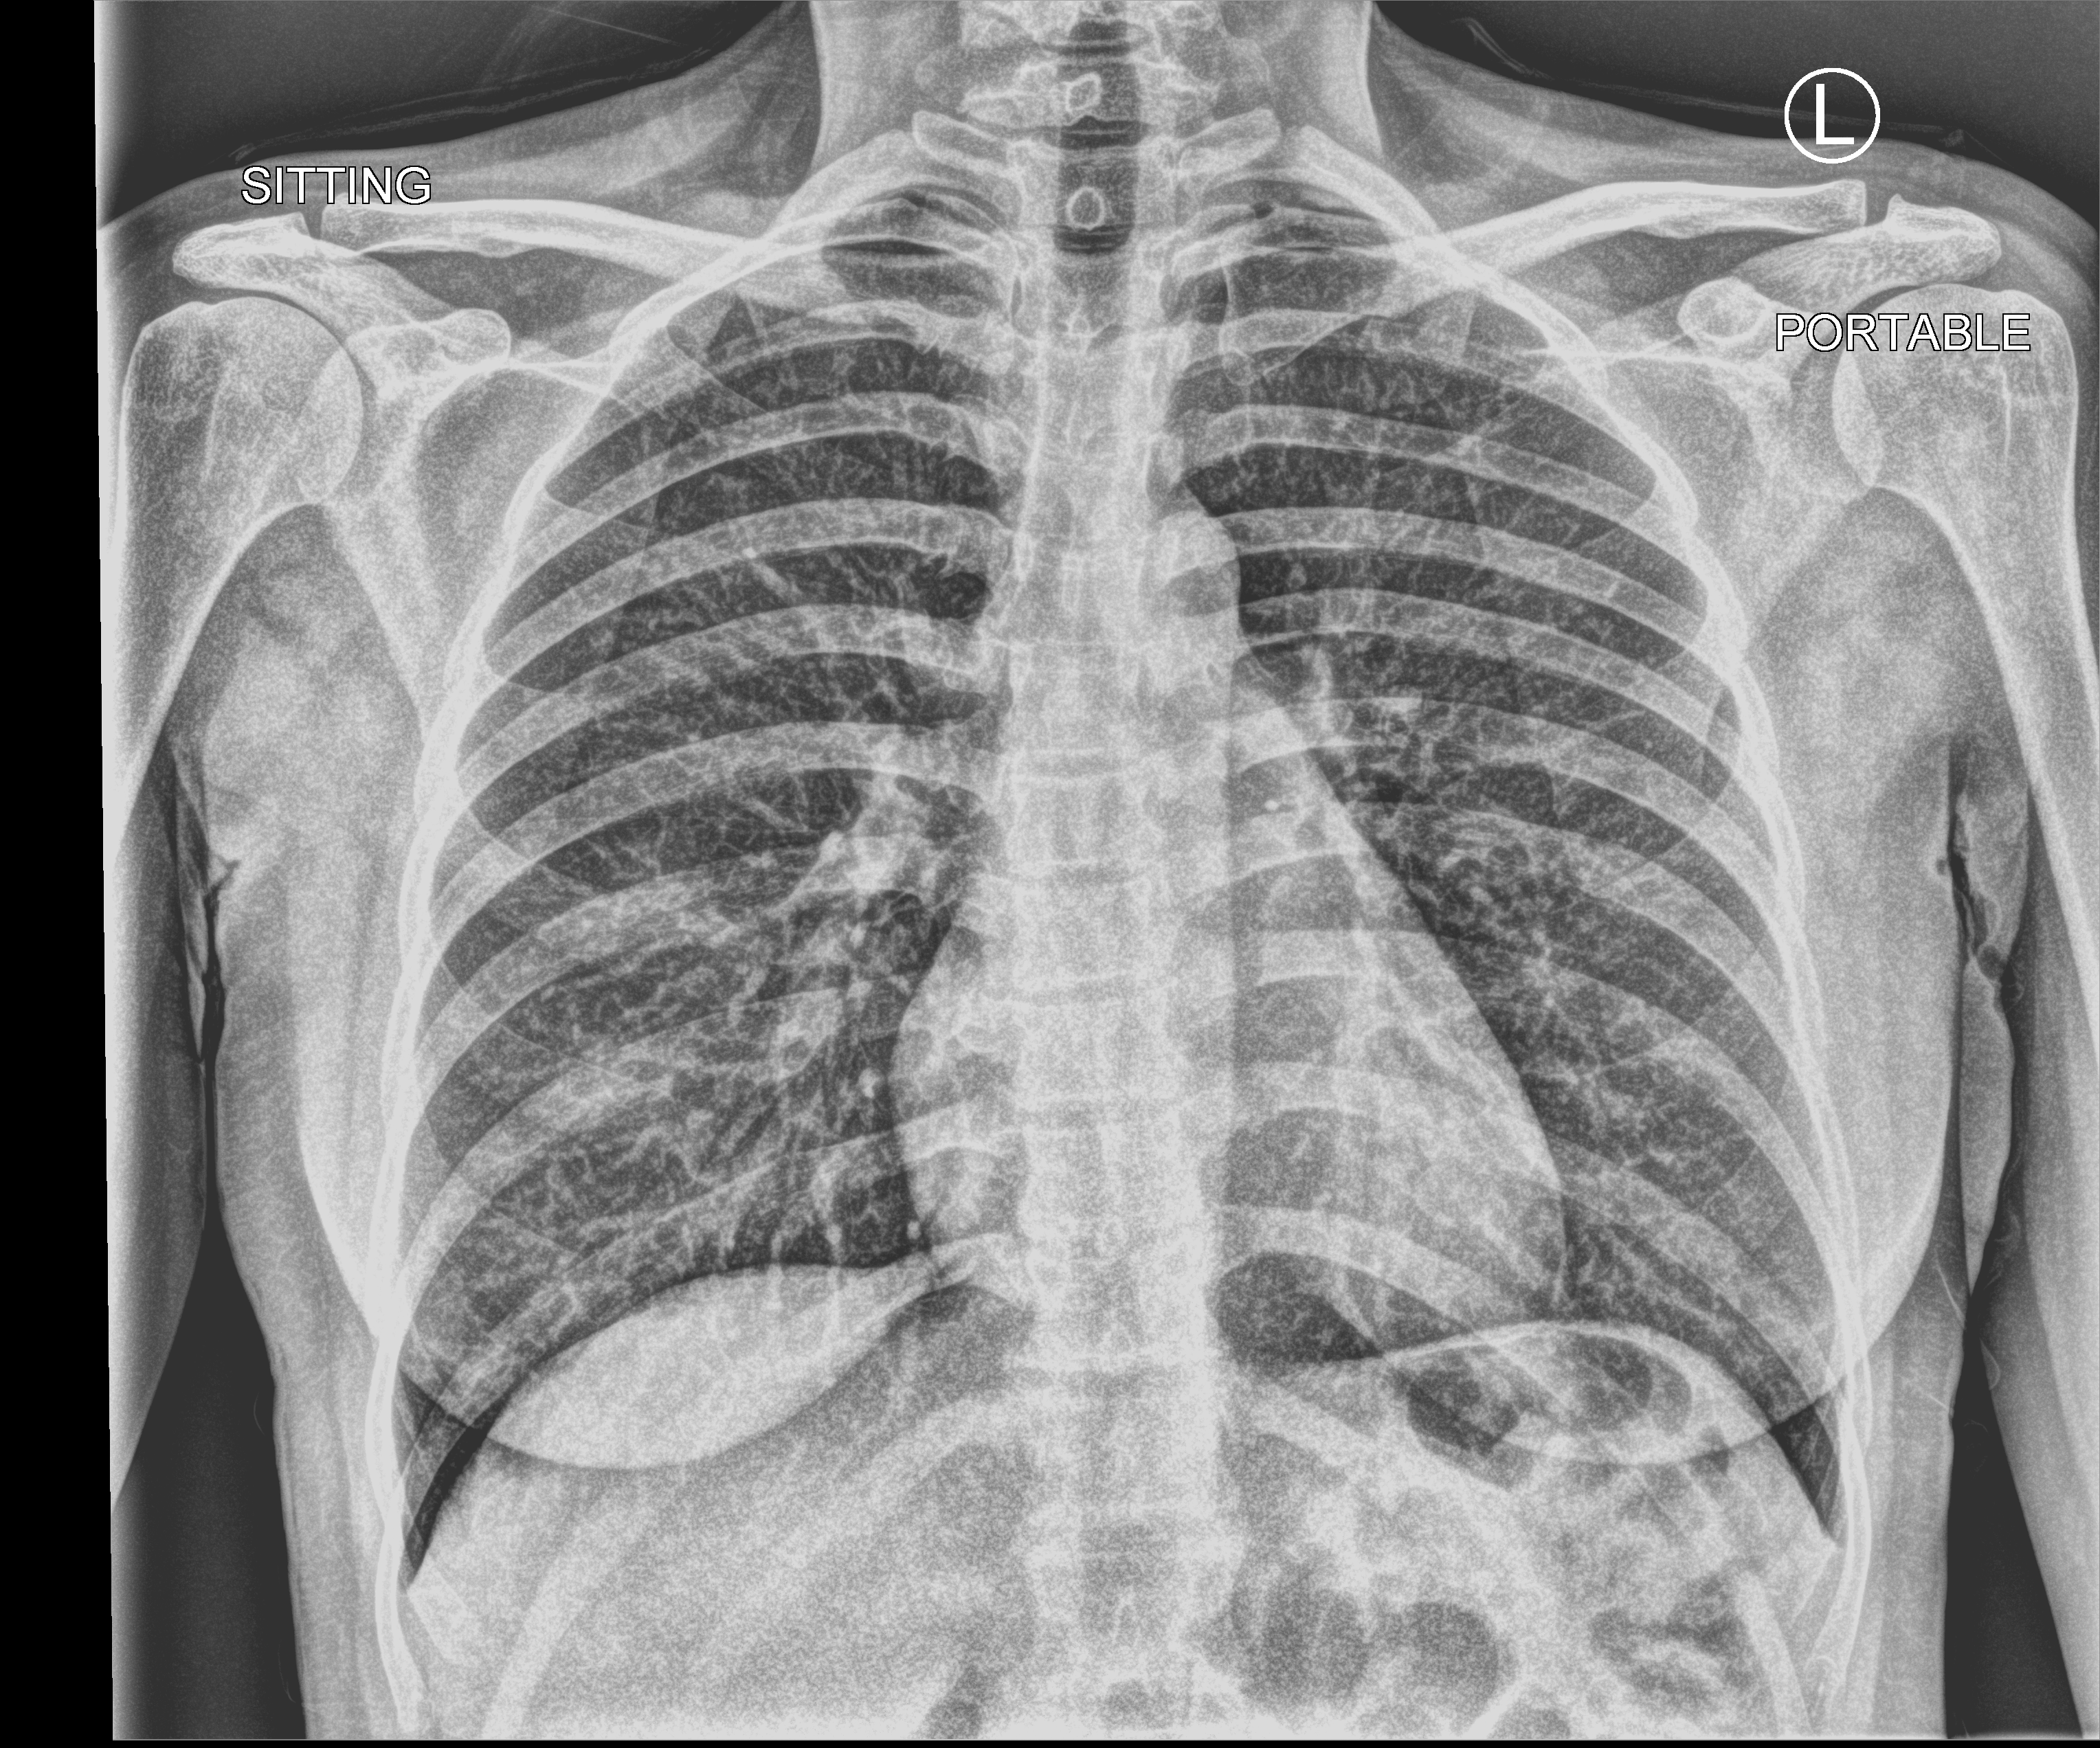
Portable chest radiograph, anteroposterior (AP) projection. Patient hospitalised with COVID-19; female, aged 18–59 years.
From the hospital-stay record, not from the radiograph (when in the stay this image was taken is not recorded):
- mechanically ventilated during this hospital stay: no
- admitted to intensive care during this hospital stay: no
- length of hospital stay: 1 day